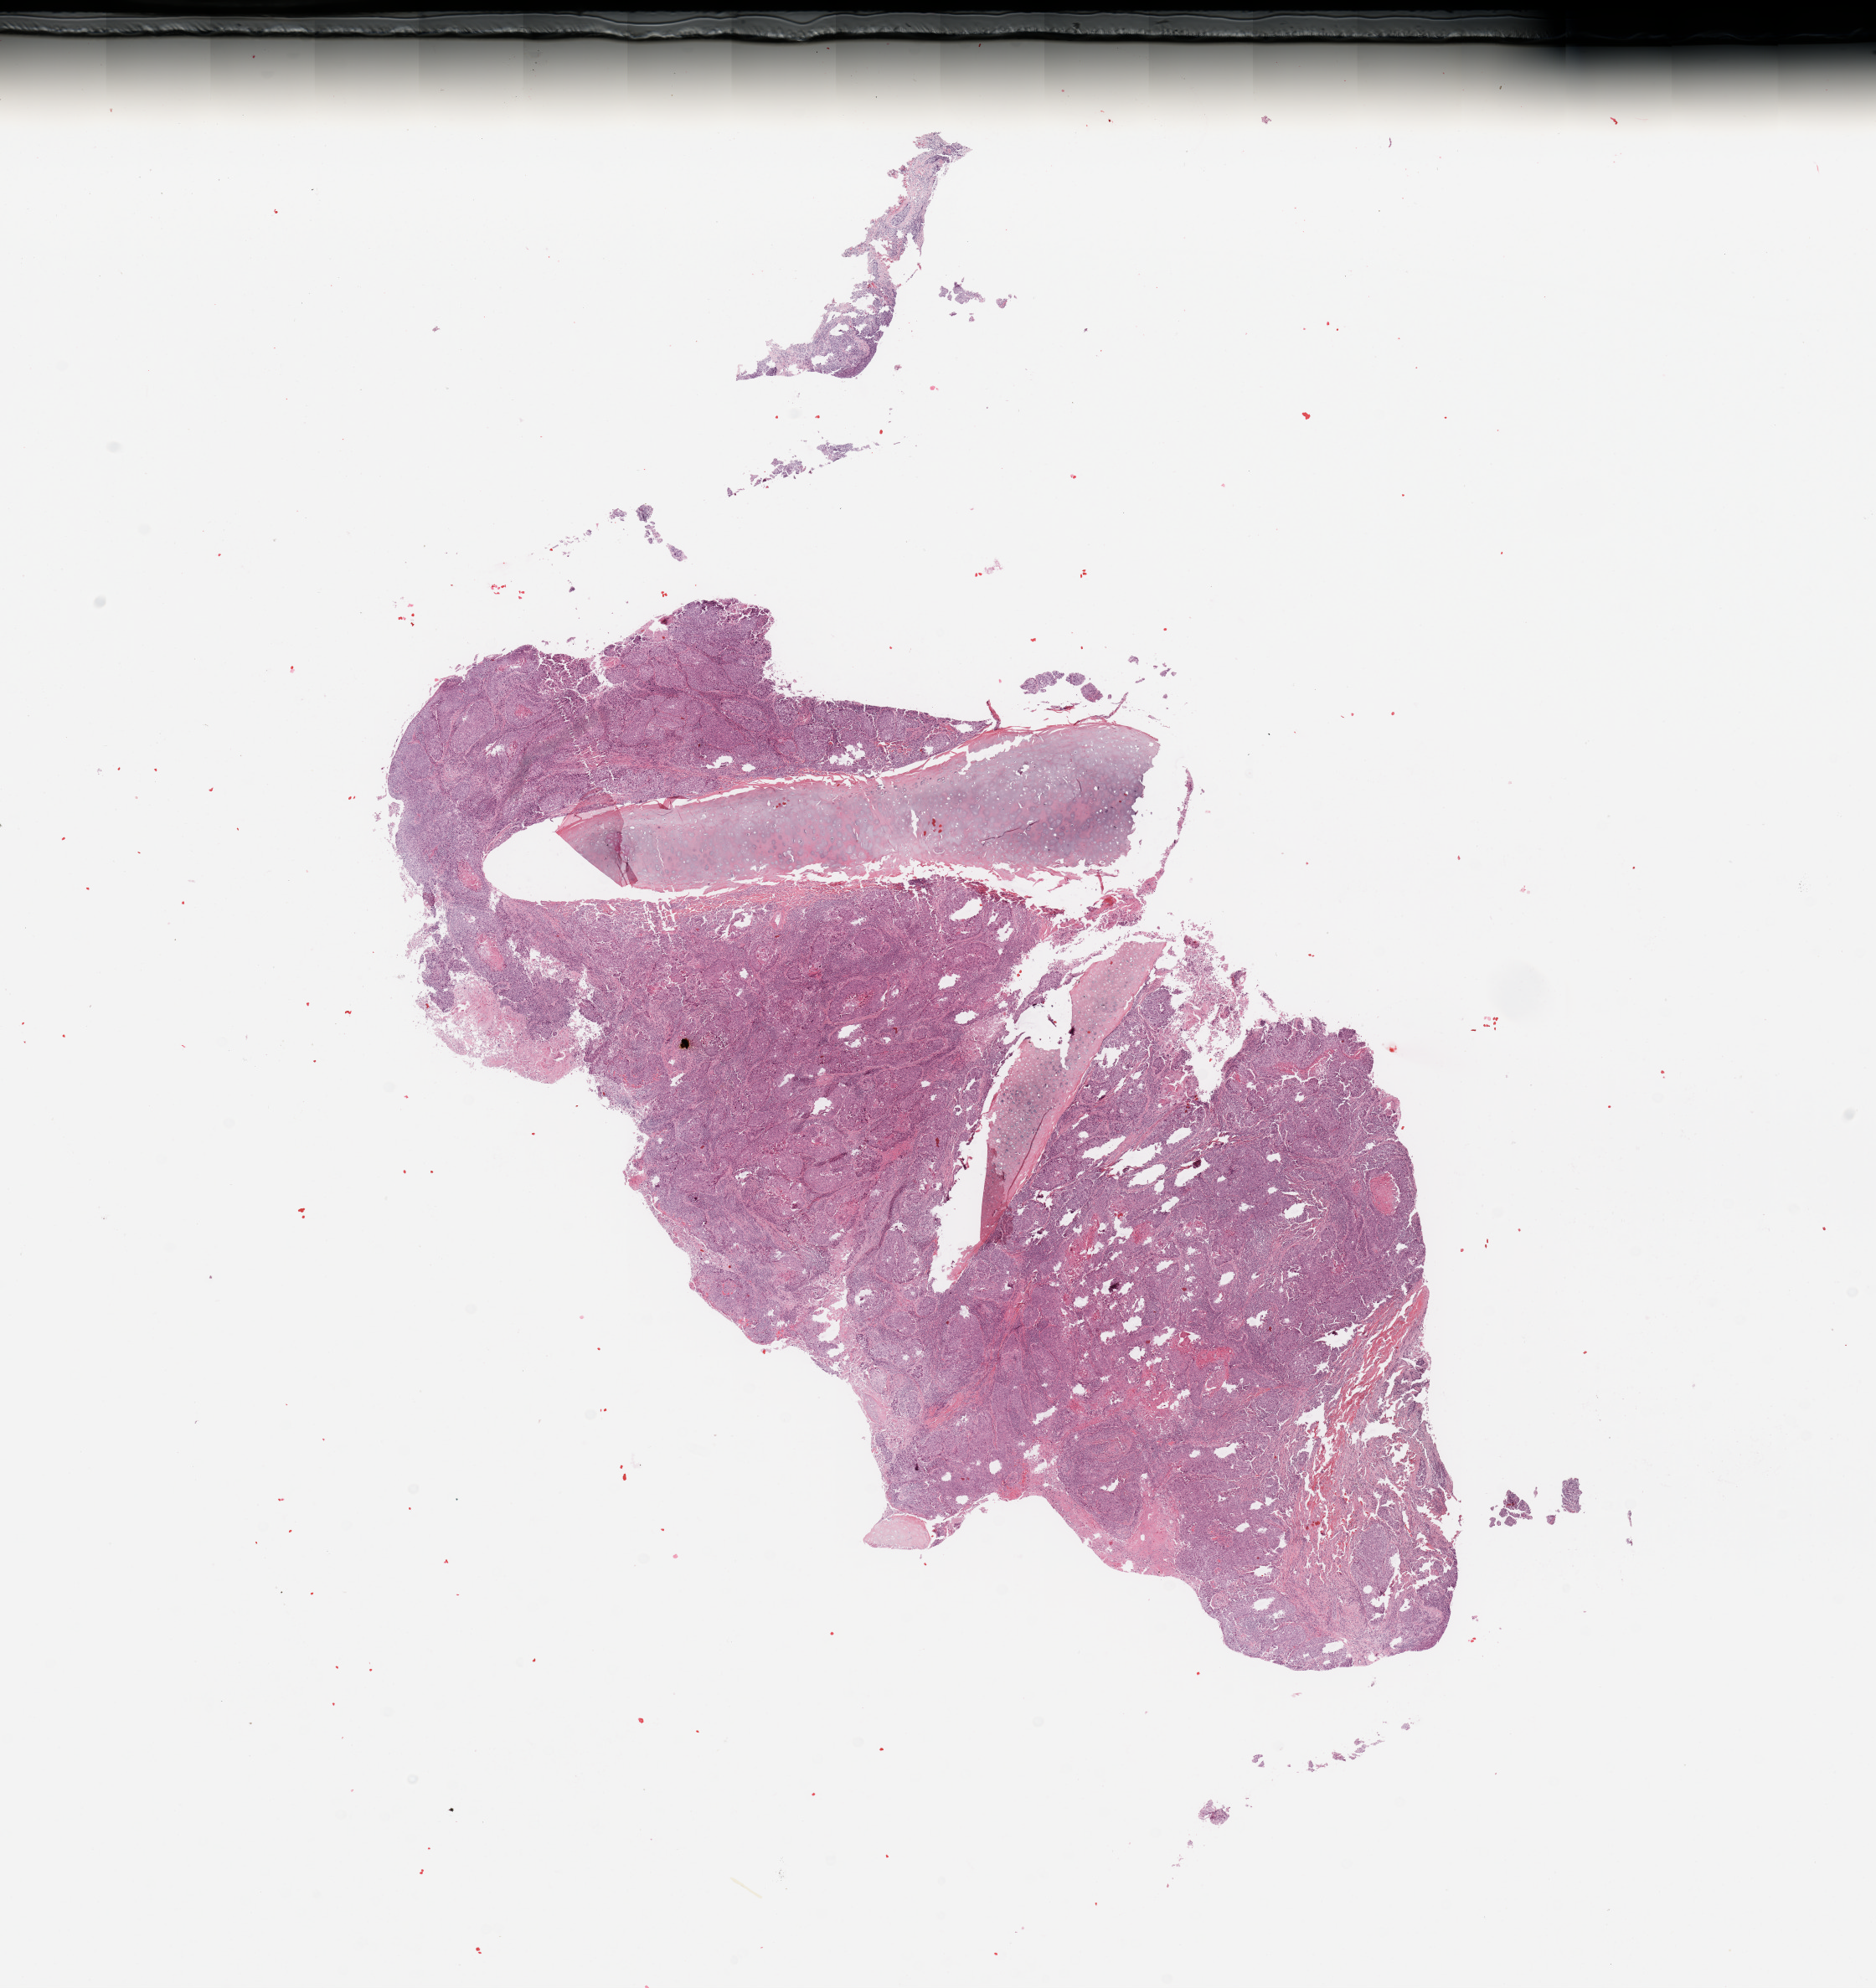
Whole-slide histology image, H&E, a low-resolution overview of the entire scanned area, about 17.7 x 18.8 mm, tumour tissue sample, sampled site: lung. Patient: male, age 76 years. Histologic grade: G2 (moderately differentiated). Slide review estimates, as recorded: tumour nuclei 85%, necrosis 5%.
* primary tumour site (as recorded): left upper lobe
* AJCC pathologic stage: IIB
* diagnosis: Squamous cell carcinoma, NOS